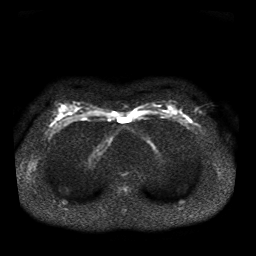
Breast MRI, one axial slice. Slice 22 of 41 in the series (ordered by position). Diffusion-weighted series; image 2 of 4 stored at this slice position (different b-values; order by instance number). 1.5 T. 5 mm slice thickness. 256 × 256 image matrix. Female patient.
Annotated regions visible in this slice (expert manual segmentation):
- tumour on diffusion-weighted imaging: bounding box <183,115,189,120> (left, top, right, bottom; pixels)